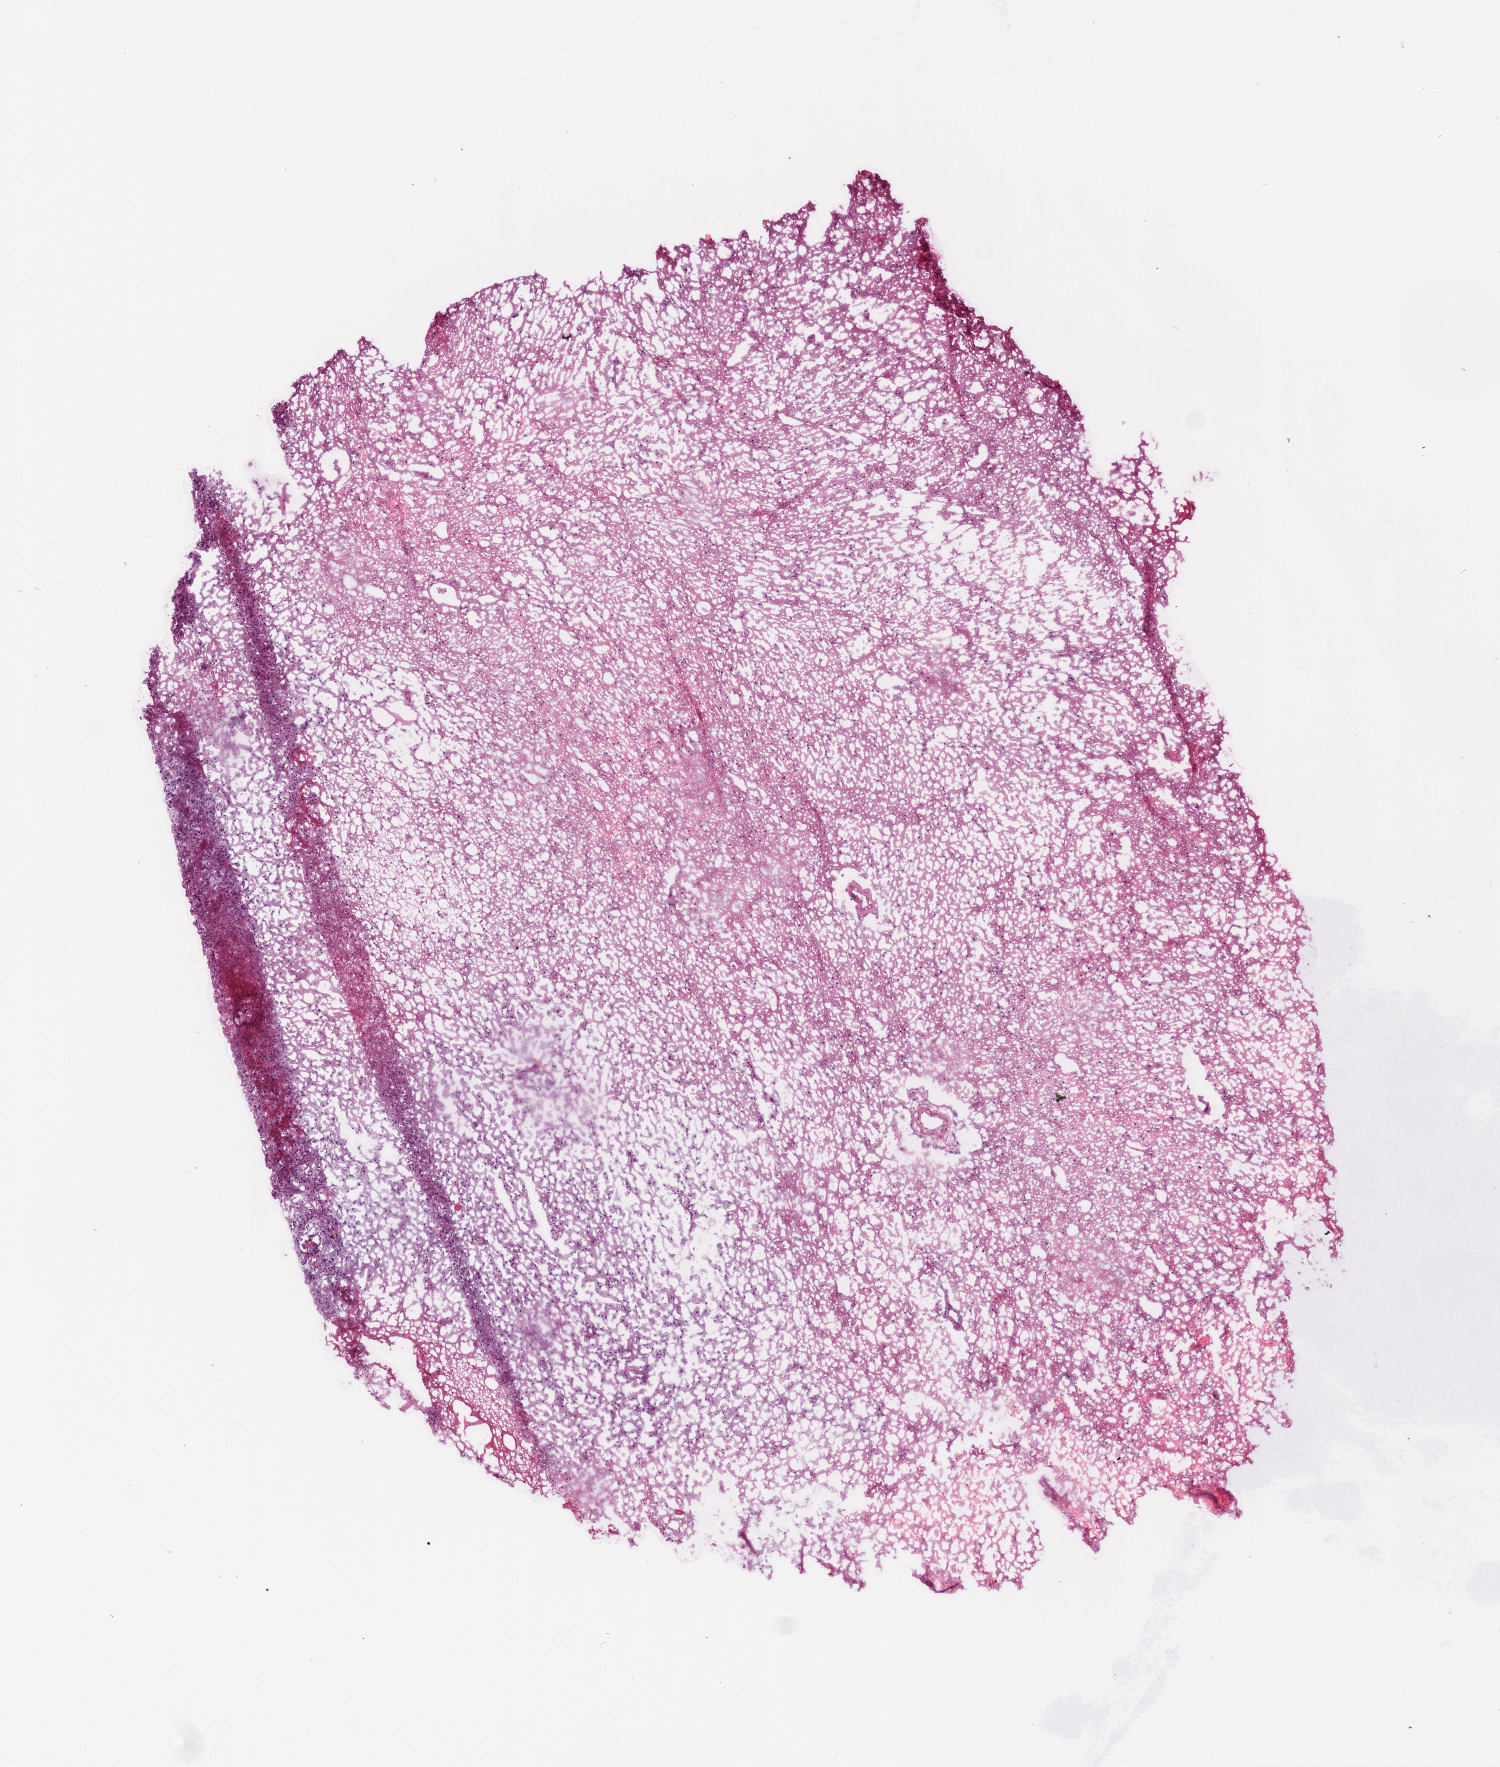
H&E whole-slide image, low-resolution overview of the scanned area, about 6.0 x 7.1 mm (from a 20x scan). Pathologist review of this section (percent, as recorded): tumour cells 90%, tumour nuclei 60%, normal cells 0%, stromal cells 0%, necrosis 10%.
Specimen: frozen section from the top of the tissue portion; primary tumour sample from the brain.